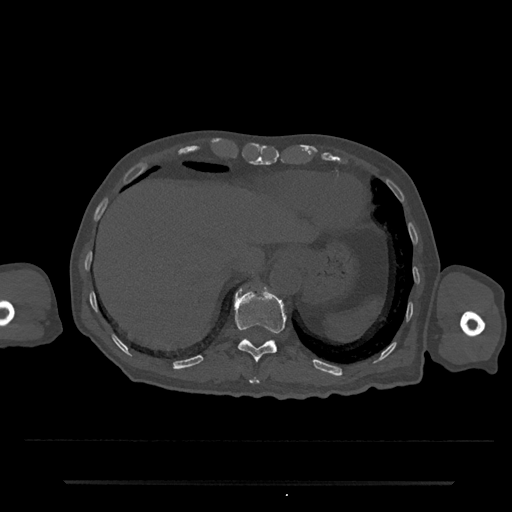
CT including the spine, one axial slice. Reconstruction kernel Br40s/3. Bone window (W 1800 / L 400 HU). 0.5 mm slice thickness. 512 × 512 image matrix, field of view 427 × 427 mm. Patient: male, 74 years. Case-level facts recorded for this patient, not image findings: primary cancer: prostate.
Structures marked on this image (semi-automatically segmented with operator editing):
- T10 vertebra: bounding box (x1, y1, x2, y2) in pixels: (249, 377, 260, 385)
- T11 vertebra: (234, 288, 286, 362)